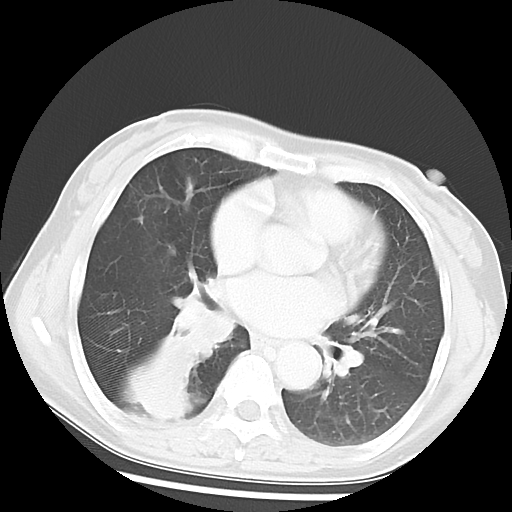
Chest CT, one axial slice; slice 27 of 52 in the series (ordered by position); lung window (W 1500 / L -600 HU); 5 mm slice thickness; 512 × 512 image matrix. Female patient, age 54 years. Case-level facts recorded for this patient, not image findings: clinical TNM (as recorded): T1c N0 M0; histopathological grade: G1-2.
Annotated regions visible in this slice (bounding box drawn by a radiologist):
- lung tumour (recorded histology: squamous cell carcinoma): box from (x=169, y=289) to (x=237, y=365) px